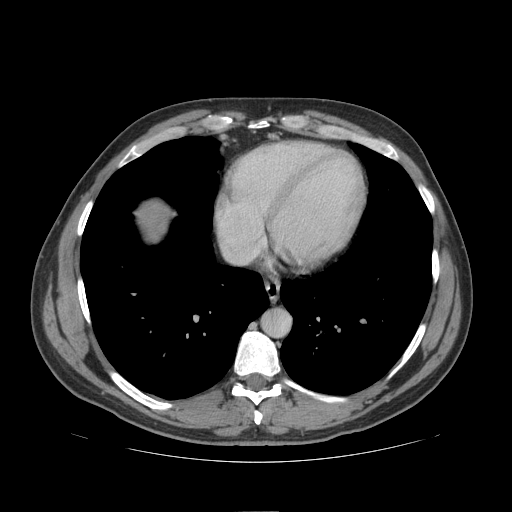
Contrast-enhanced abdominal CT (liver protocol), one axial slice. Slice 99 of 109 in the series (ordered by position). Reconstruction kernel STANDARD. 140 kVp. Soft-tissue window (W 400 / L 40 HU). 2.5 mm slice thickness. 512 × 512 image matrix. From the clinical record (not read from this slice): diagnosis: hepatocellular carcinoma (patient treated with transarterial chemoembolisation; whether this scan precedes or follows treatment is not stated here); TNM stage (as recorded): Stage-IIIB; Child-Pugh class: A; tumour nodularity: multinodular.
Annotated regions visible in this slice (semi-automatic segmentation, software-assisted and operator-edited):
- liver parenchyma outside the tumour (the mass and vessels are separate outlines, so this box may not span the whole liver): box from (x=138, y=202) to (x=170, y=240) px